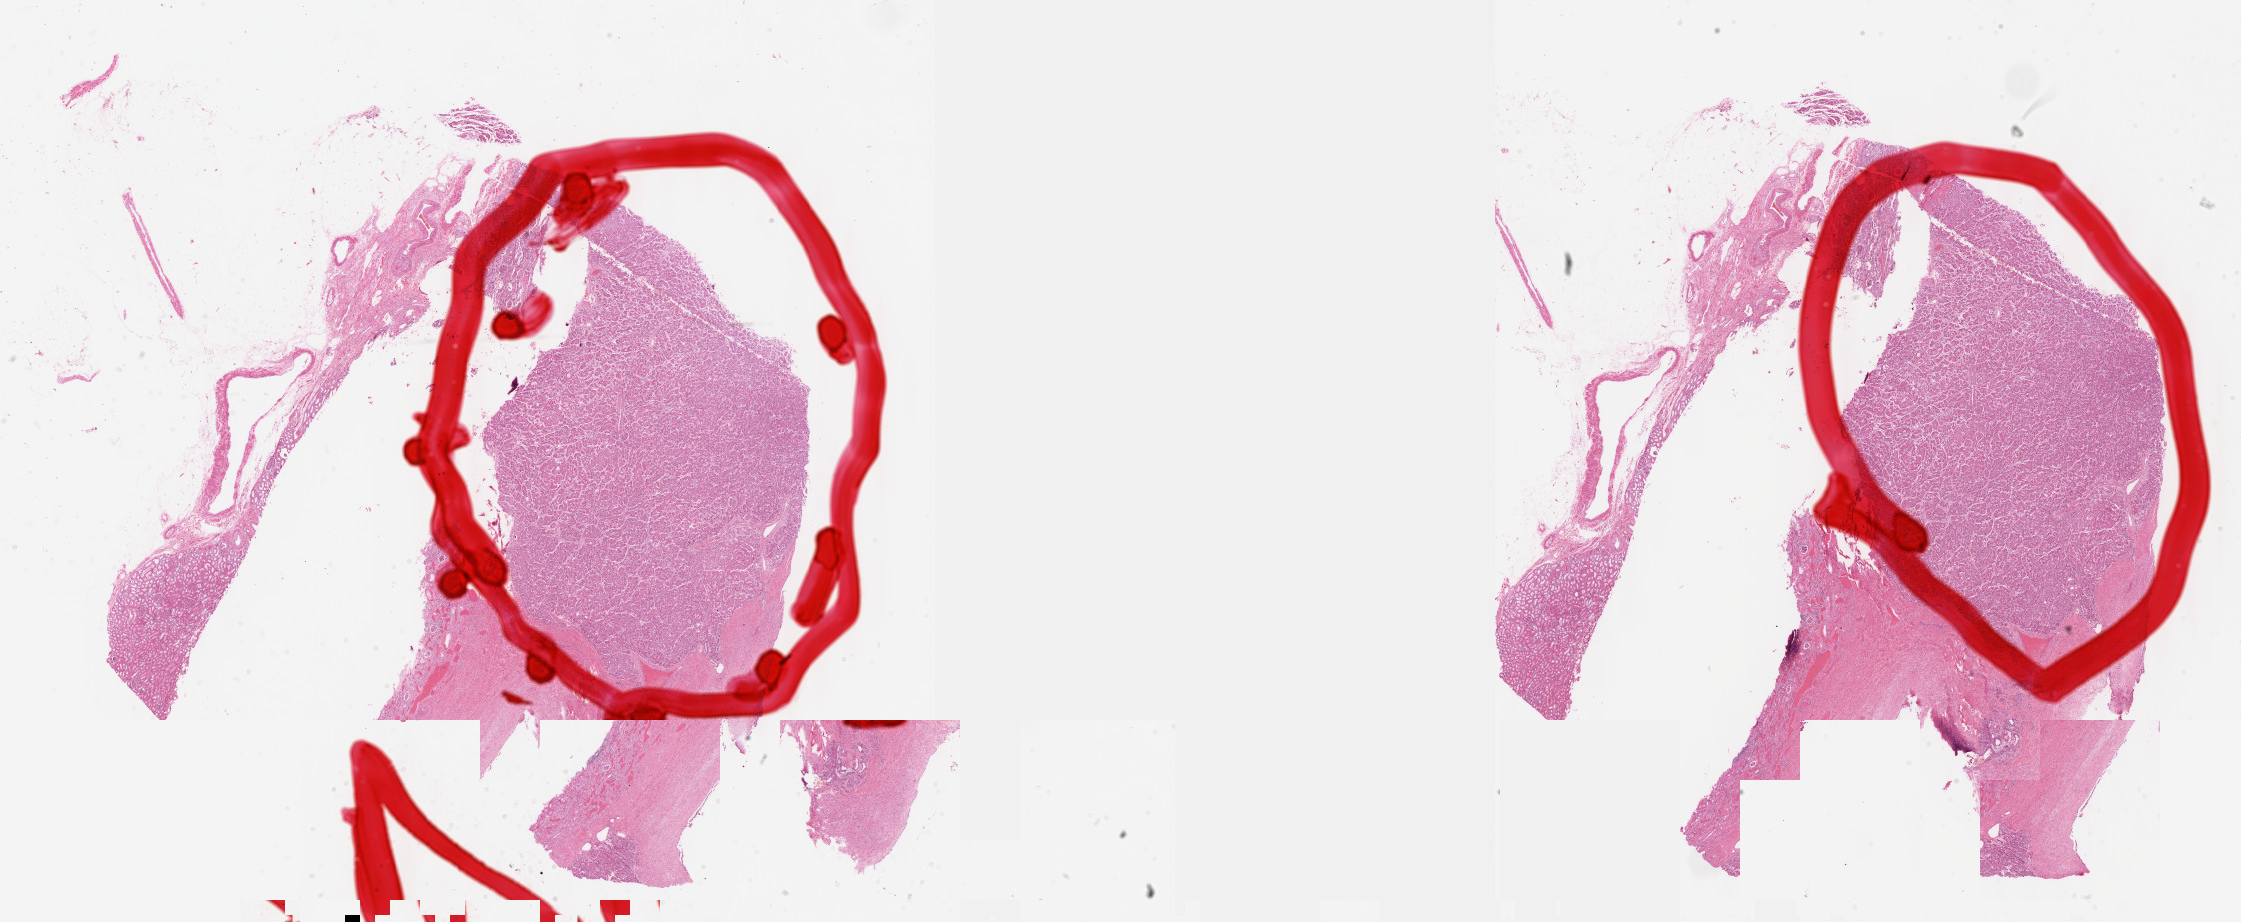
H&E whole-slide image, whole scanned area (about 36.2 x 14.9 mm, acquisition: 40x scan) shown as a low-resolution overview; formalin-fixed paraffin-embedded (FFPE) diagnostic section; sample: primary tumour, kidney. Male, age 18 years at initial diagnosis. Pathologist review of this section (percent, as recorded): tumour cells 85%, tumour nuclei 95%, normal cells 0%, stromal cells 15%, necrosis 0%. Inflammatory infiltration, as recorded: lymphocyte infiltration 2%, monocyte infiltration 0%, neutrophil infiltration 0%.
- diagnosis: Renal cell carcinoma, chromophobe type
- laterality: left
- lymph nodes positive (case pathology): 0 of 19 examined
- AJCC pathologic stage: II (7th edition)
- TNM: T2a N0